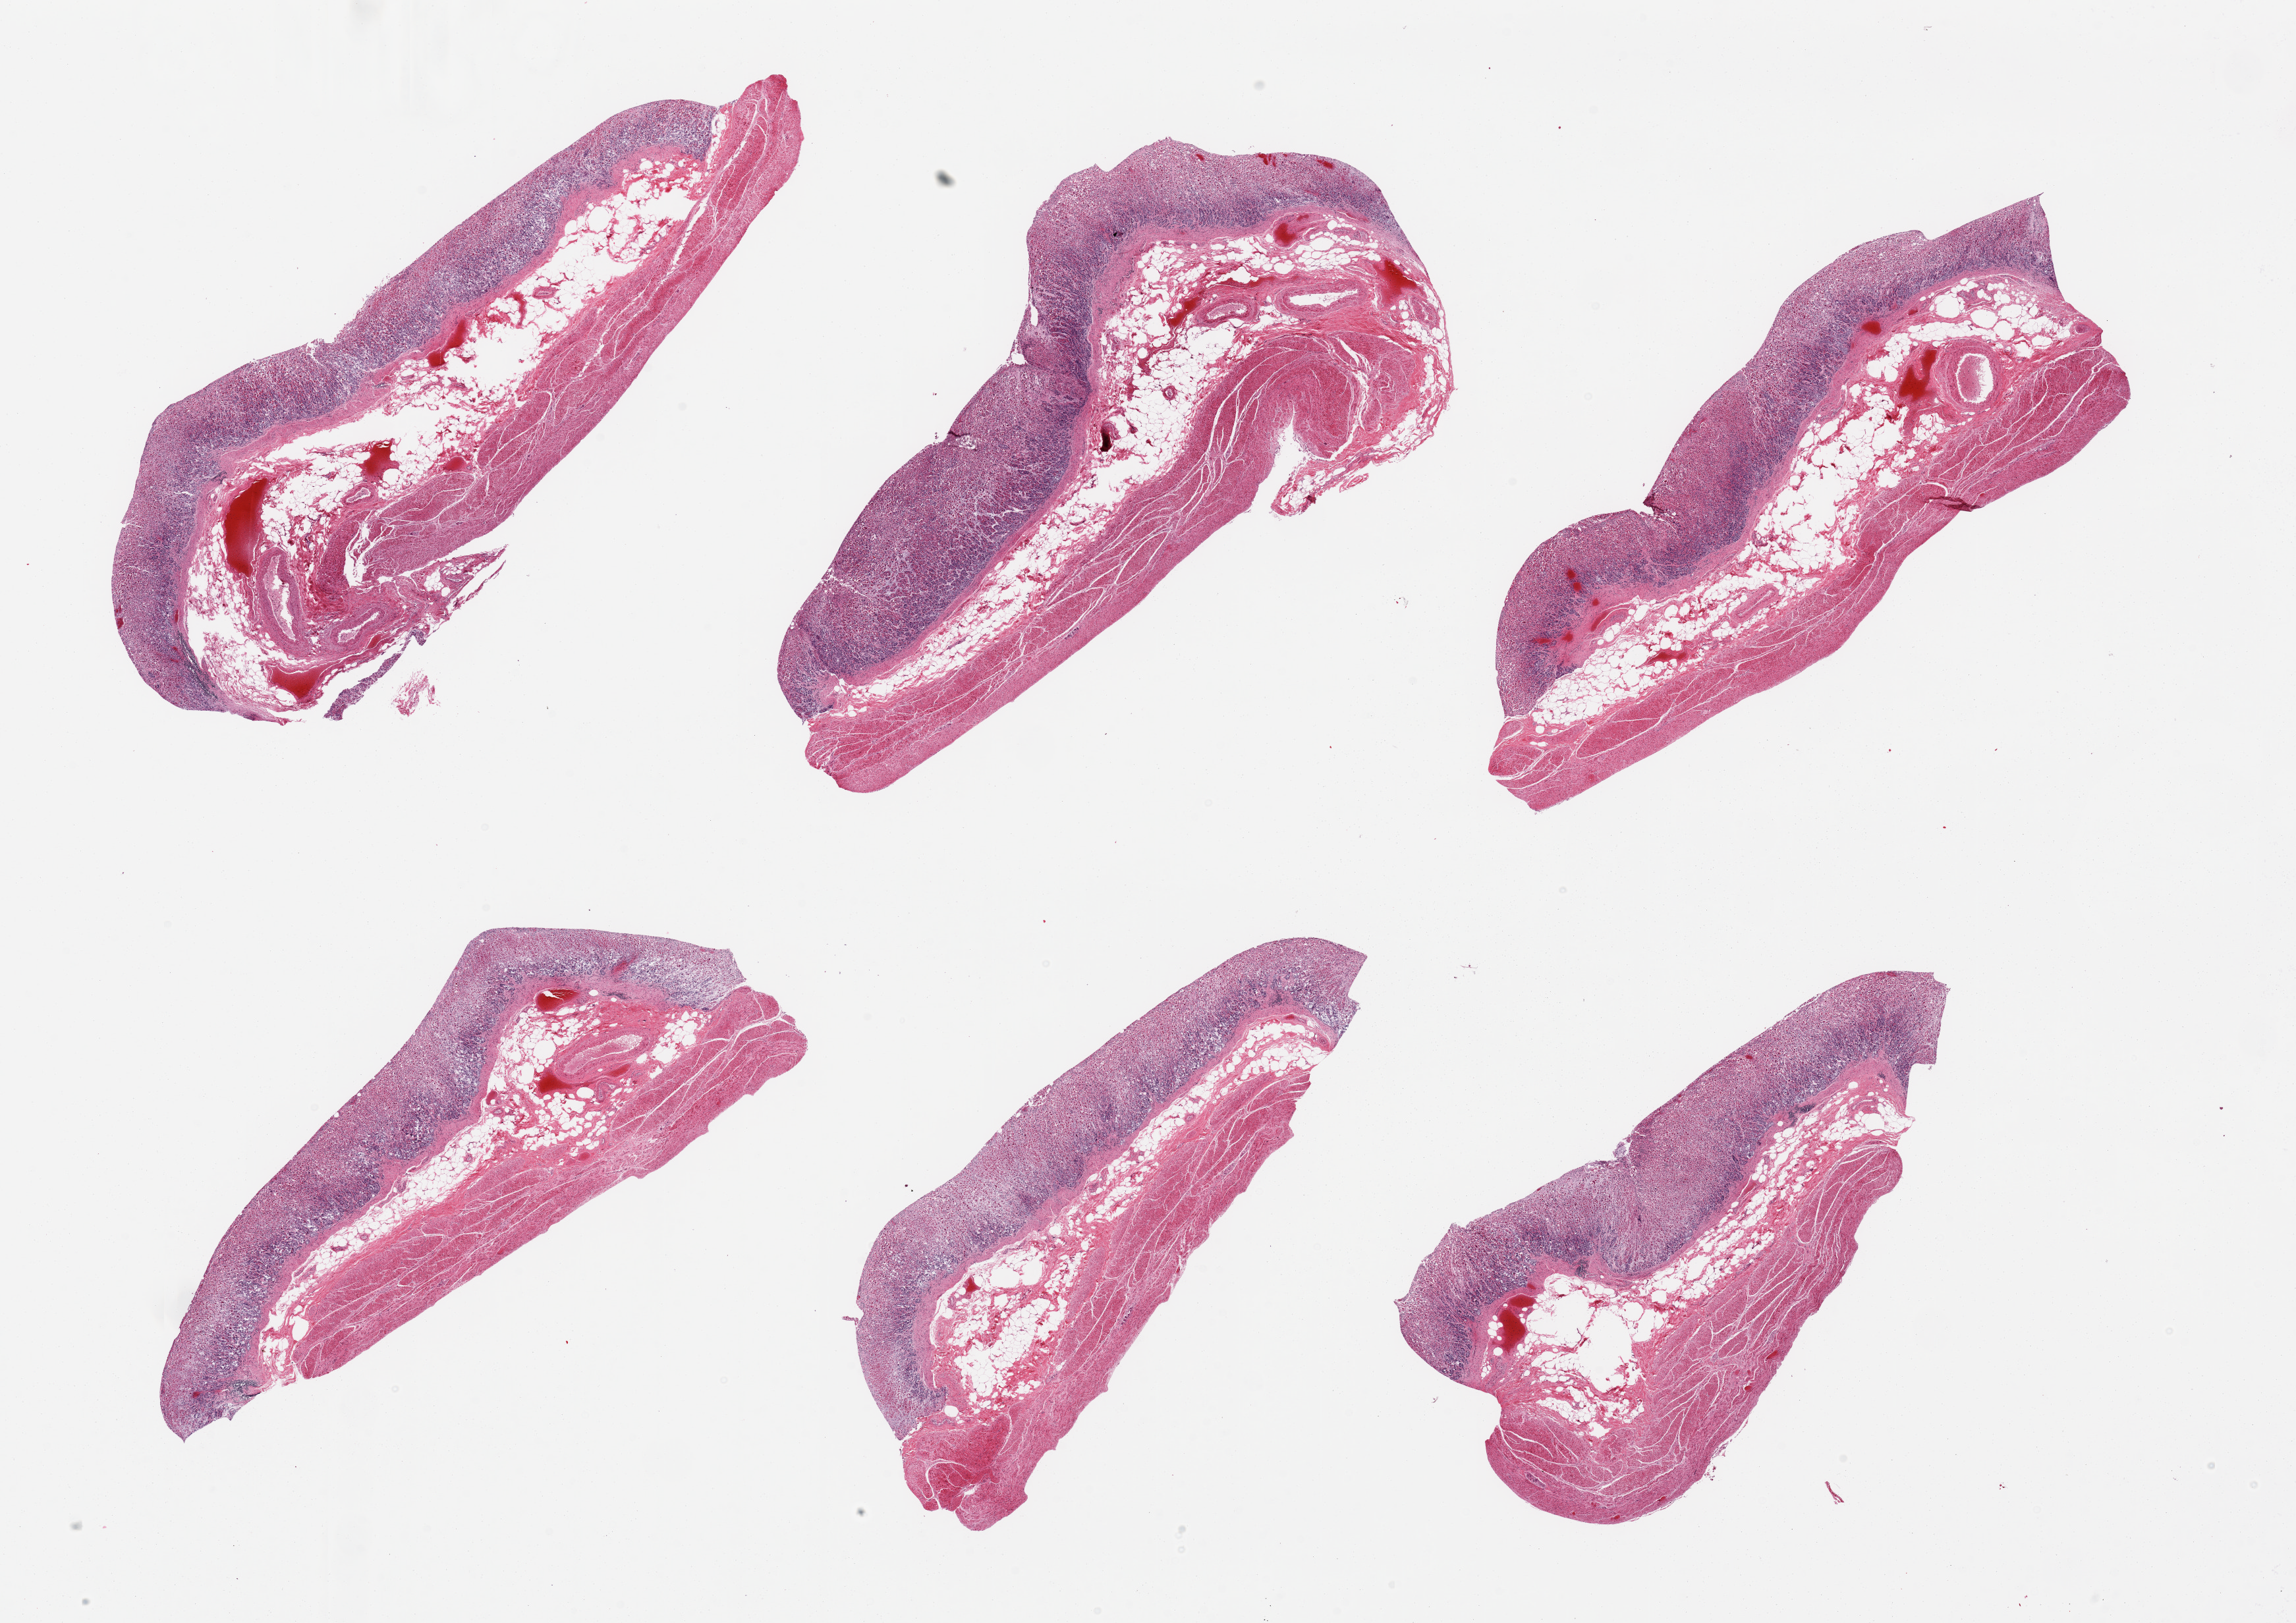
Digitized haematoxylin and eosin-stained section, brightfield — low-resolution overview of the scanned area, about 27.6 x 19.5 mm (slide scanned at 20x). PAXgene-fixed, paraffin-embedded tissue. Target tissue: stomach. Donor tissue sample. Donor: male.
Reviewer comment on this tissue sample: 6 pieces, severely autolyzed mucosa, muscularis.